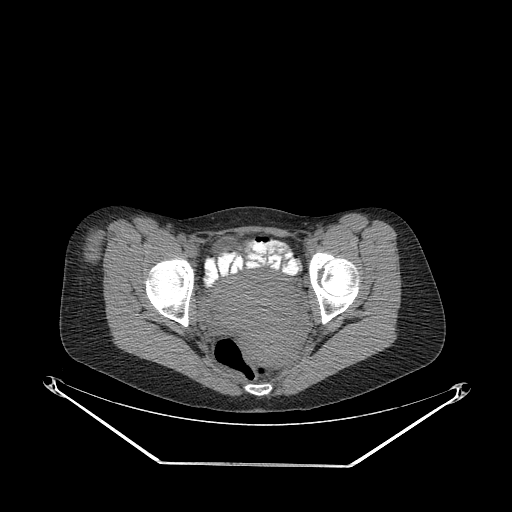
CT of an extremity soft-tissue mass (from a PET/CT study), one axial slice. Position 71 of 267 along the scan axis. Reconstruction kernel STANDARD. 140 kVp. Soft-tissue window (W 400 / L 40 HU). 3.75 mm slice thickness. 512 × 512 image matrix, field of view 500 × 500 mm. Female patient. Case-level facts recorded for this patient, not image findings: histological type: synovial sarcoma; grade: intermediate; site of the primary tumour: right thigh.
Outlined on this slice (expert contour drawn on MRI and transferred to this co-registered scan by the dataset authors):
- gross tumour volume including surrounding oedema: bounding box (x1, y1, x2, y2) in pixels: (84, 231, 110, 266)
- gross tumour volume (mass): (82, 233, 104, 266)